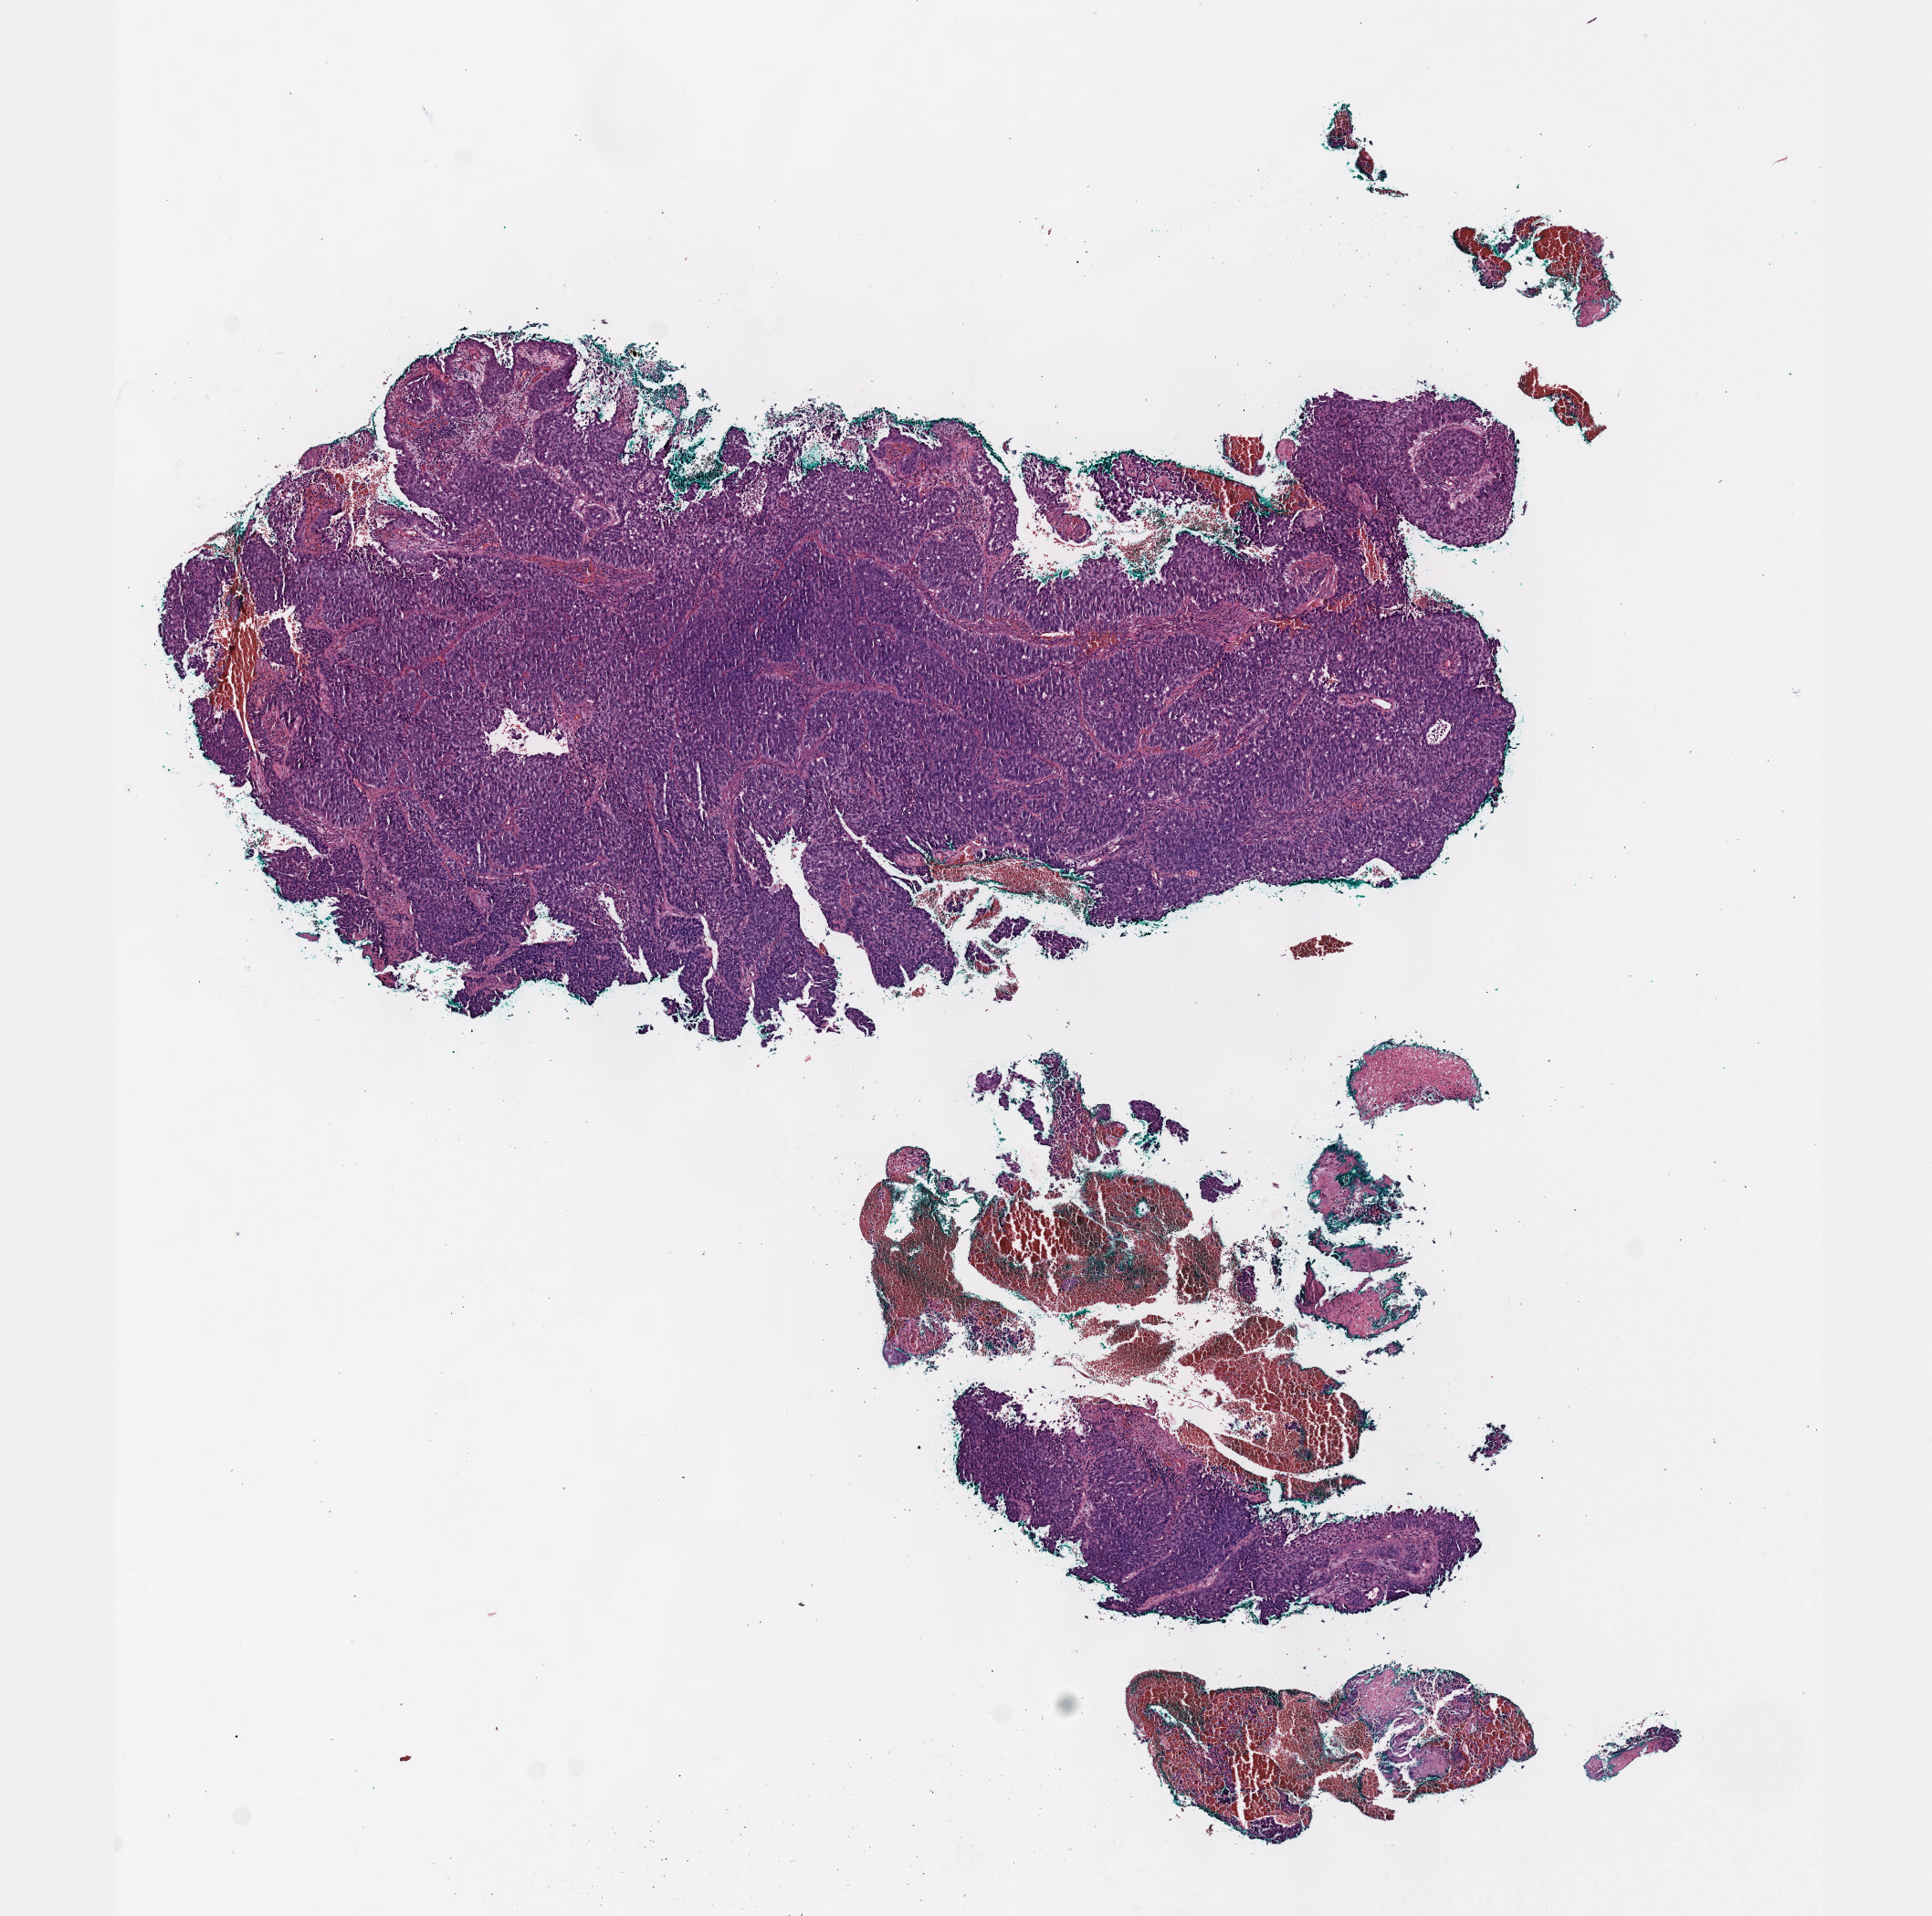
Digitized Hematoxylin and eosin (H&E) stained tissue section (whole slide), whole scanned area (about 8.6 x 8.5 mm, slide scanned at 40x) shown as a low-resolution overview, formalin-fixed paraffin-embedded (FFPE) diagnostic section, cervix, primary tumour sample. Patient: female, age at initial diagnosis 41 years. Histologic grade: GX (grade cannot be assessed).
FIGO stage: IIIB. Histologic diagnosis: Squamous cell carcinoma, NOS (cervix uteri).